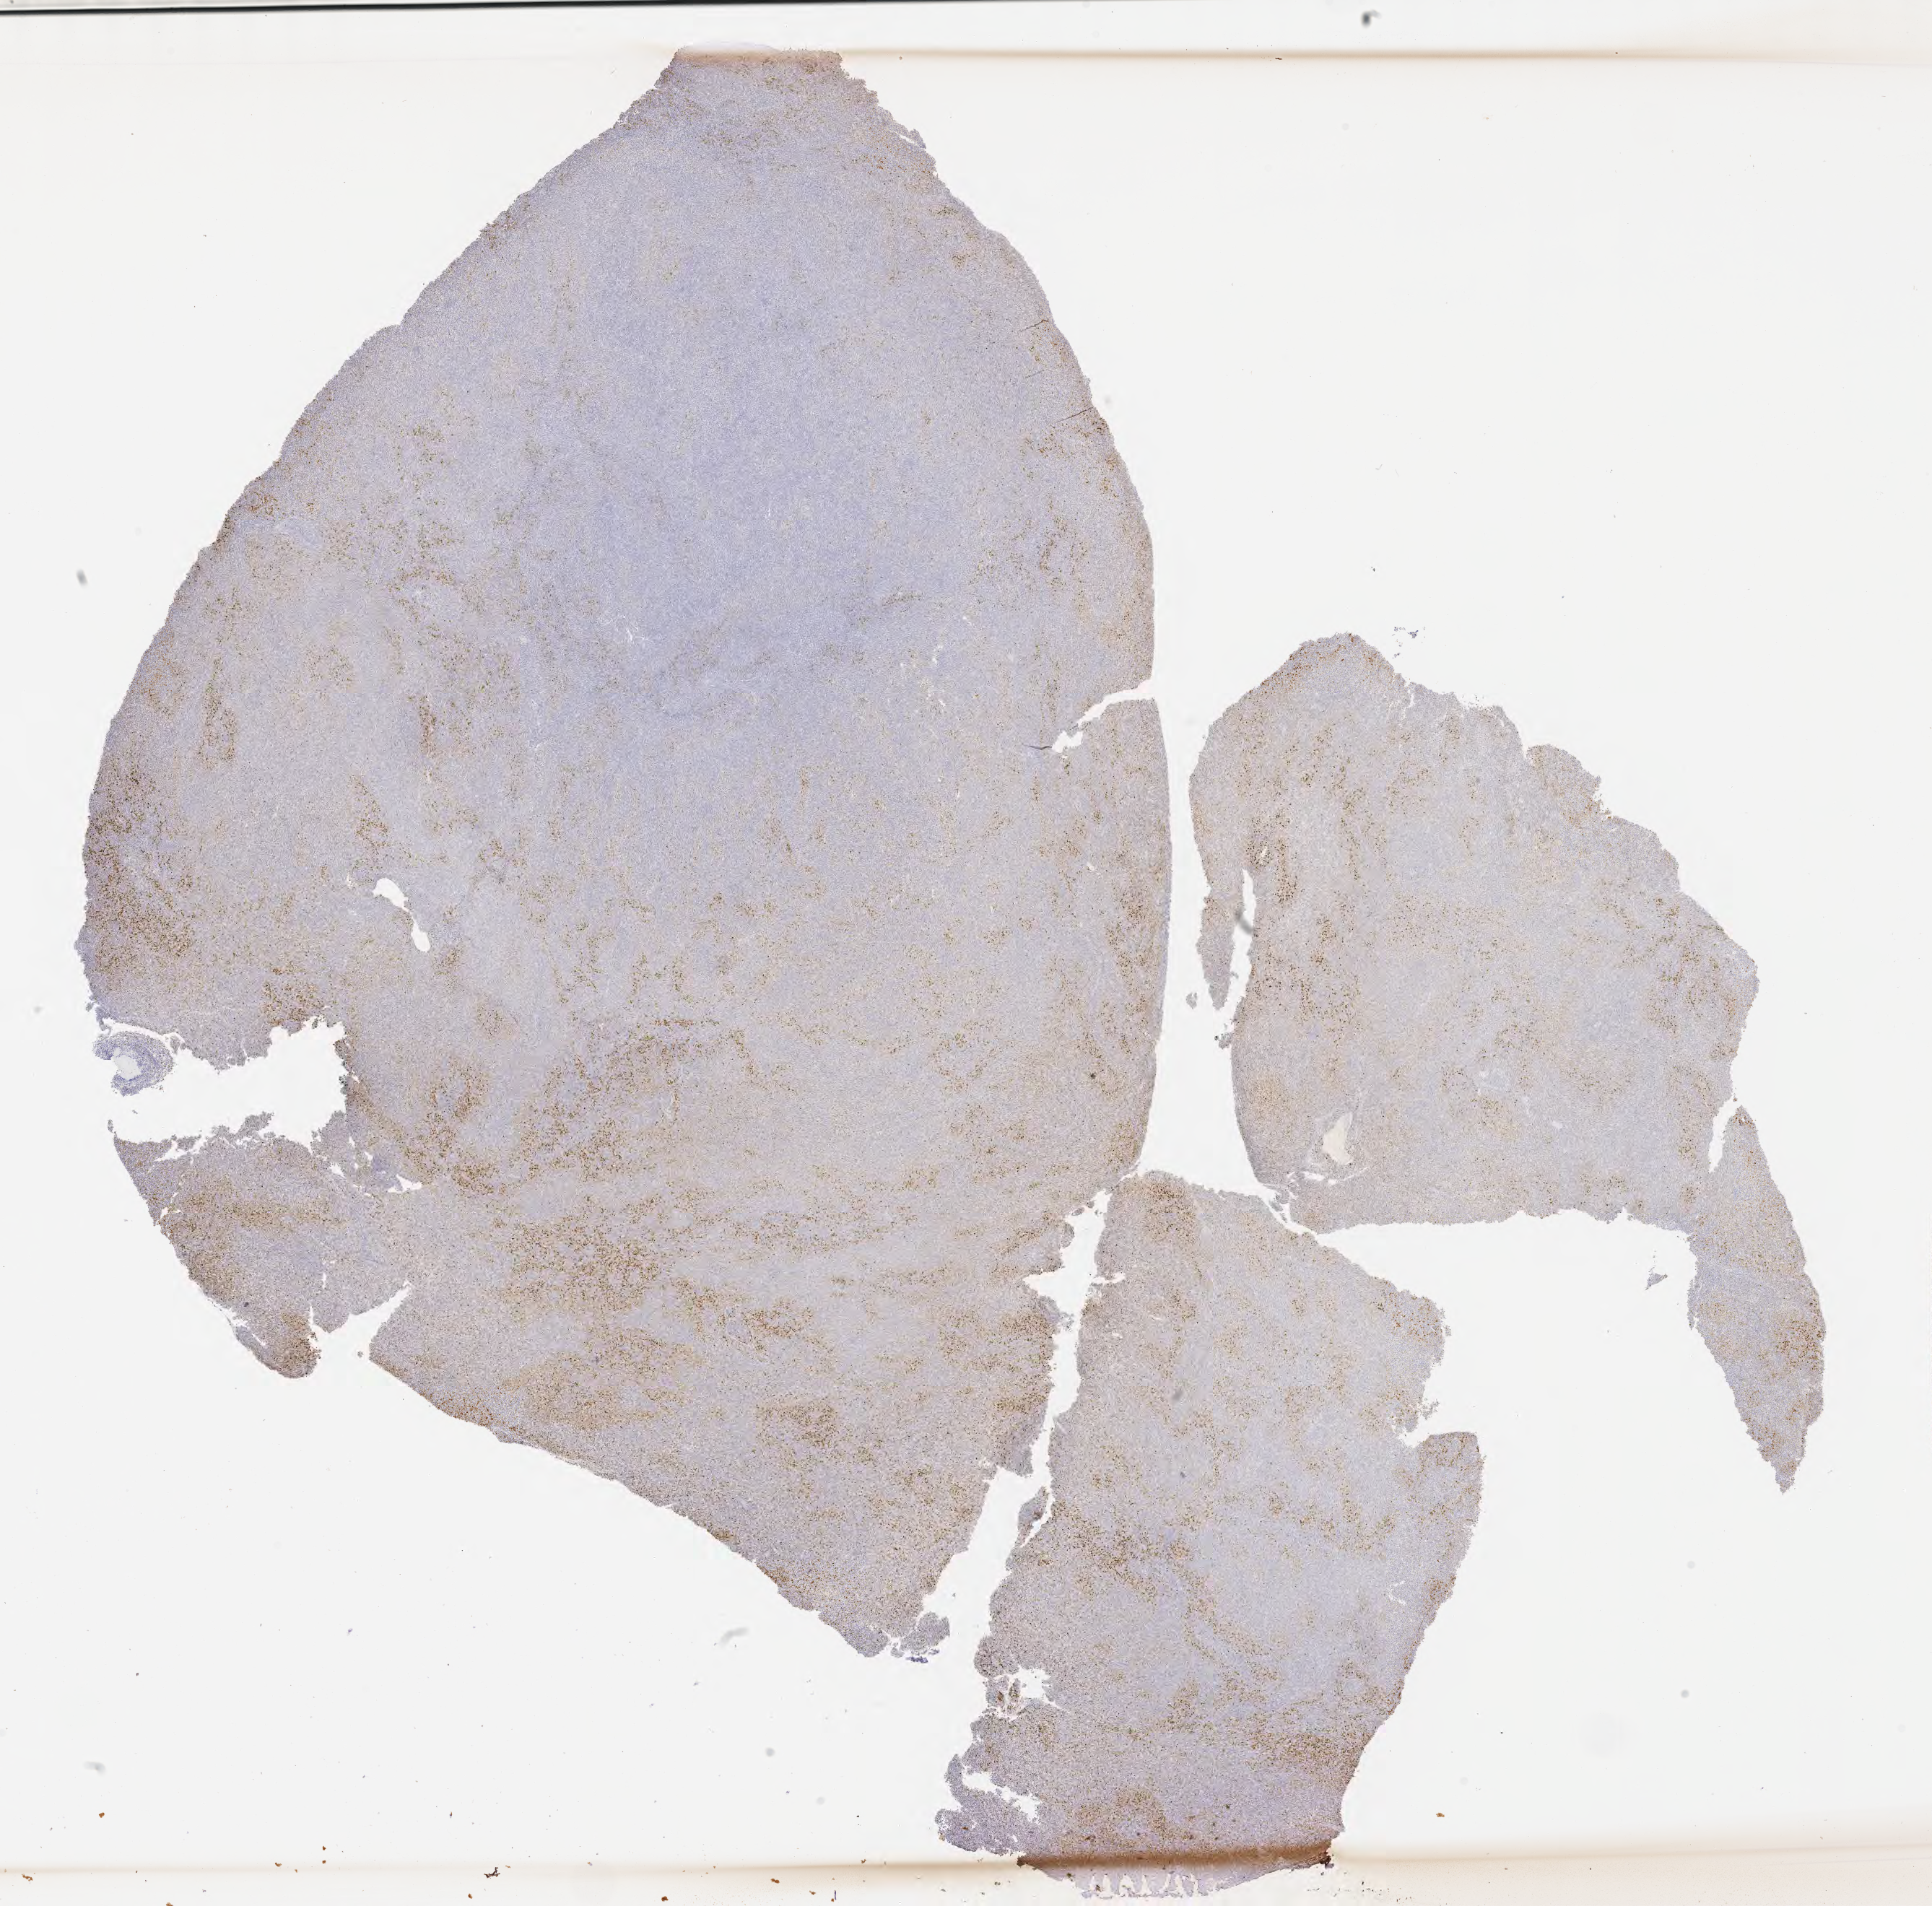
Immunohistochemistry (IHC) whole-slide image stained for IRF4/MUM1, shown as a low-resolution overview of the whole scanned area (about 21.6 x 21.3 mm); tumor tissue; site: liver. Patient female; 46 years old.
Diagnosis: Diffuse large B-cell lymphoma, NOS.